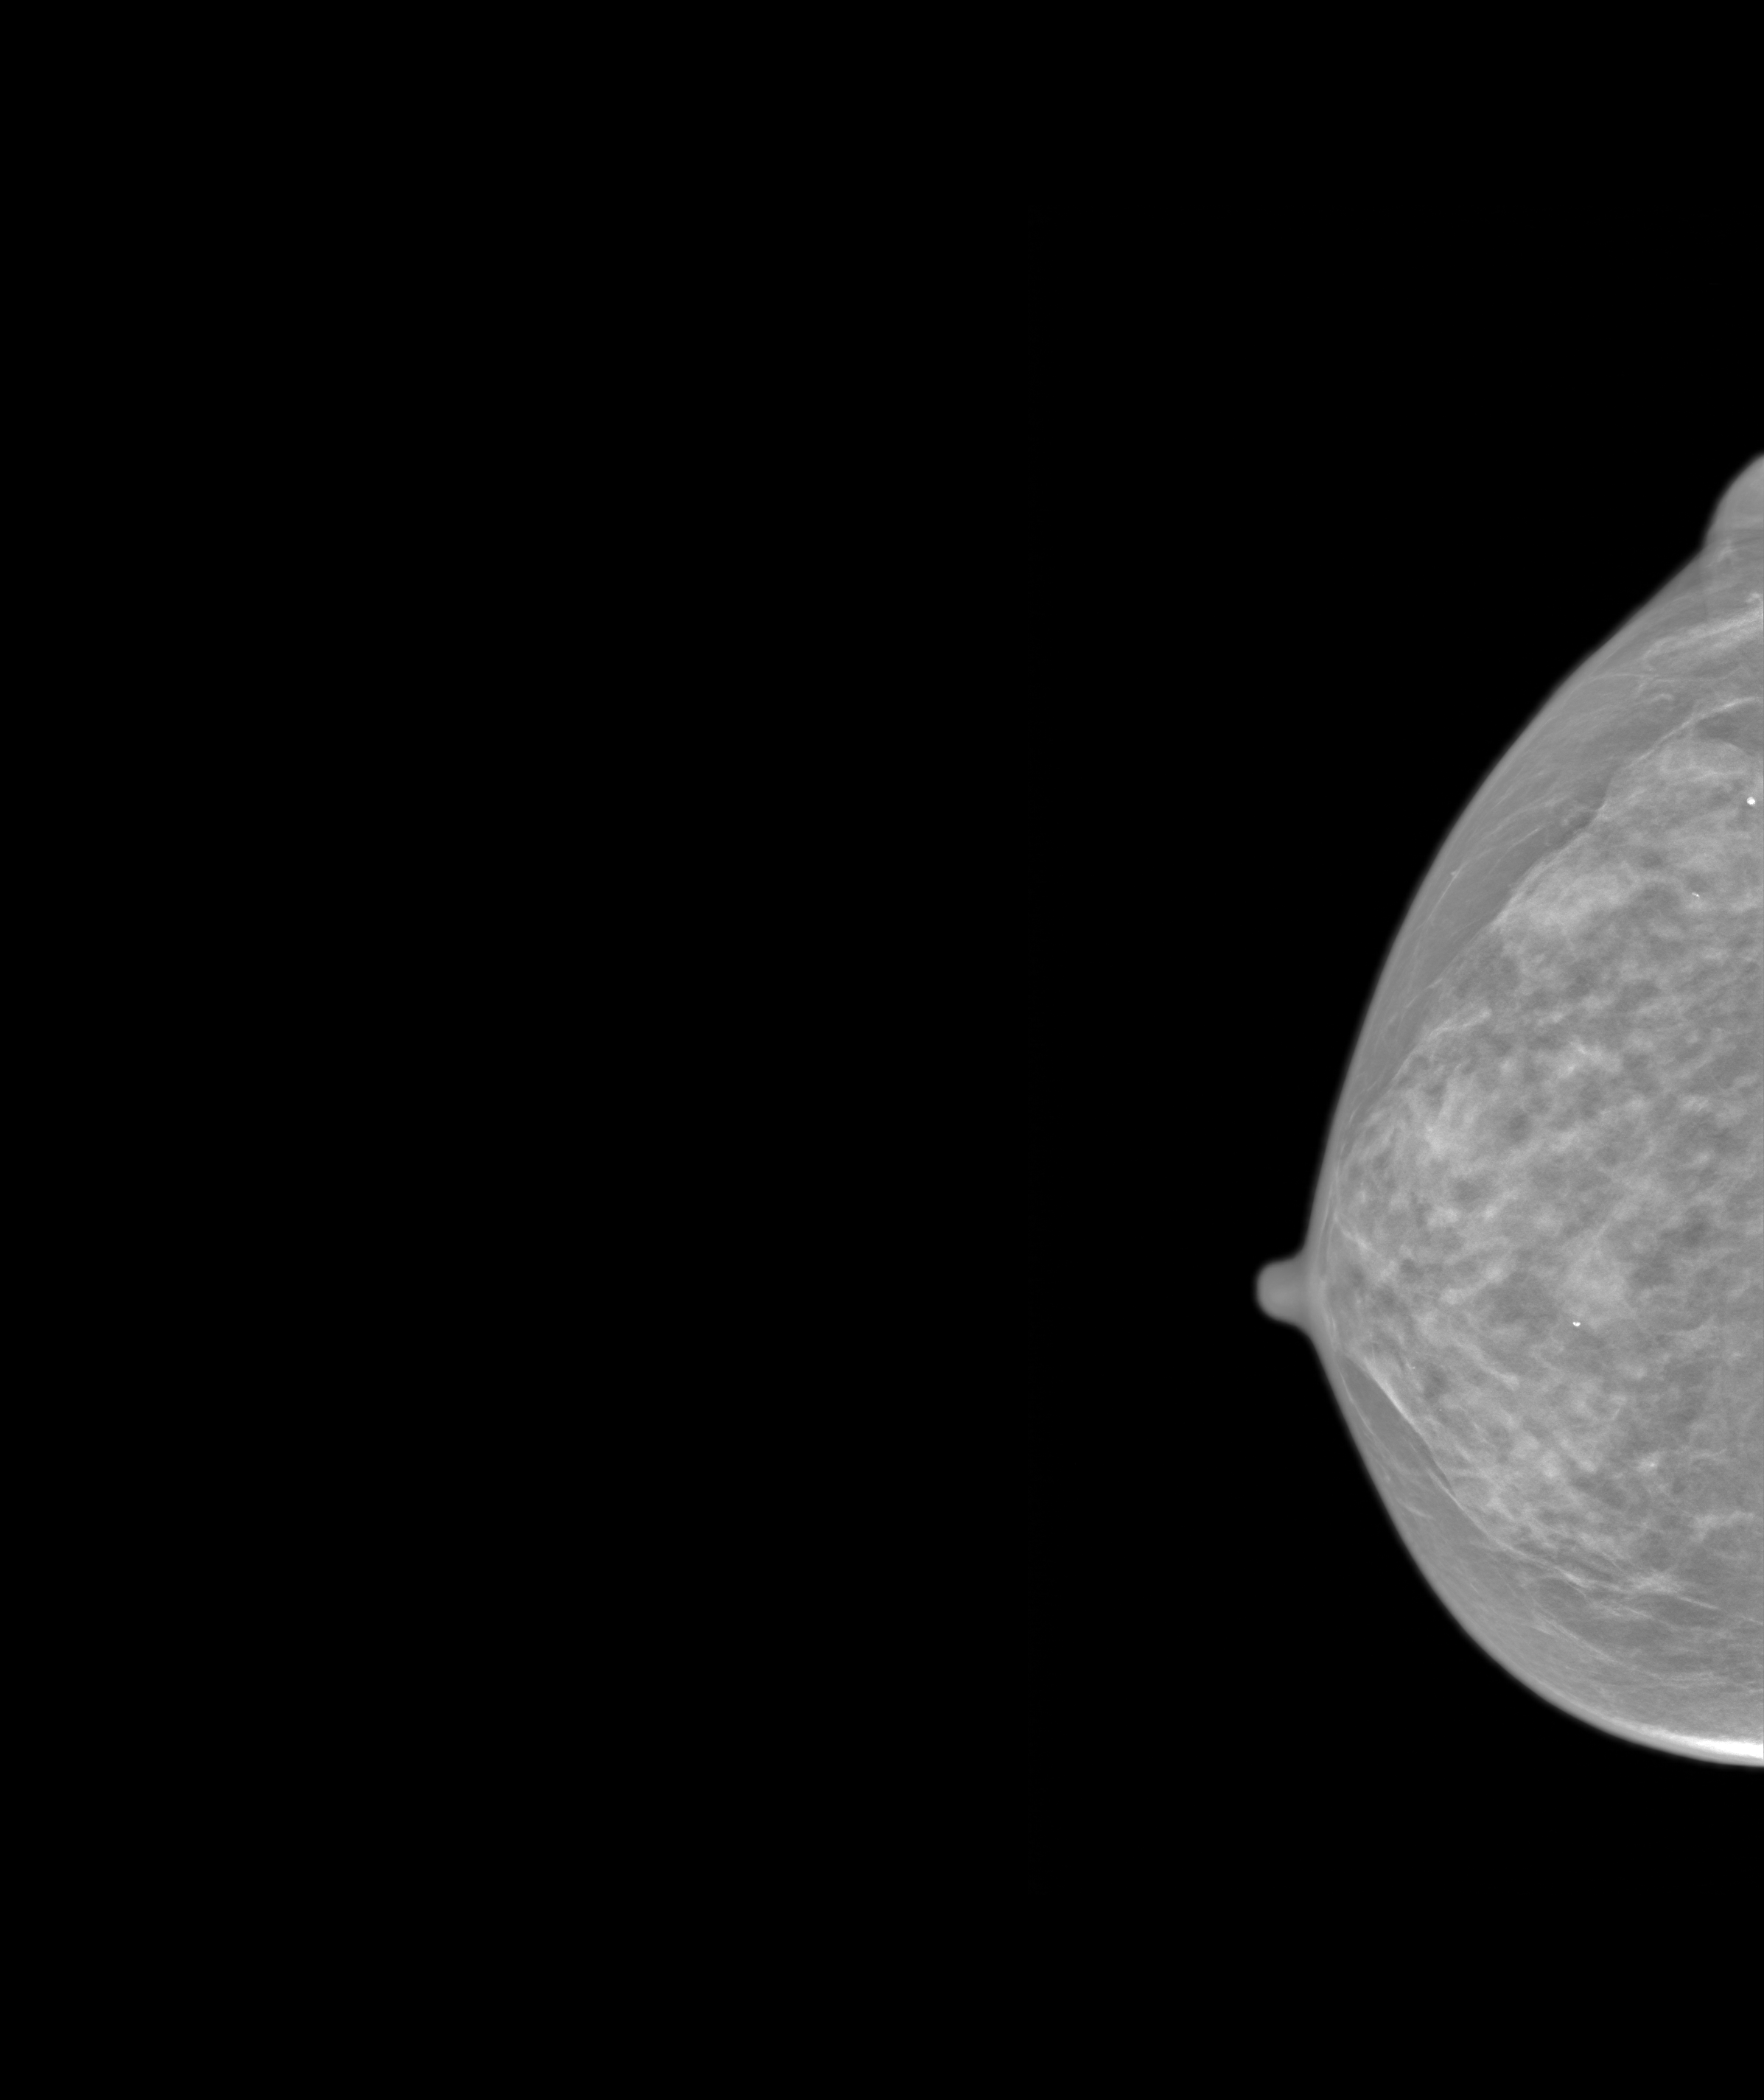
Annual screening mammography examination; system: SenoIris_1SP2(440). Patient: female, 68 years.
Image type: synthesized 2-D view from tomosynthesis. Breast: right. Projection: craniocaudal (CC) view.